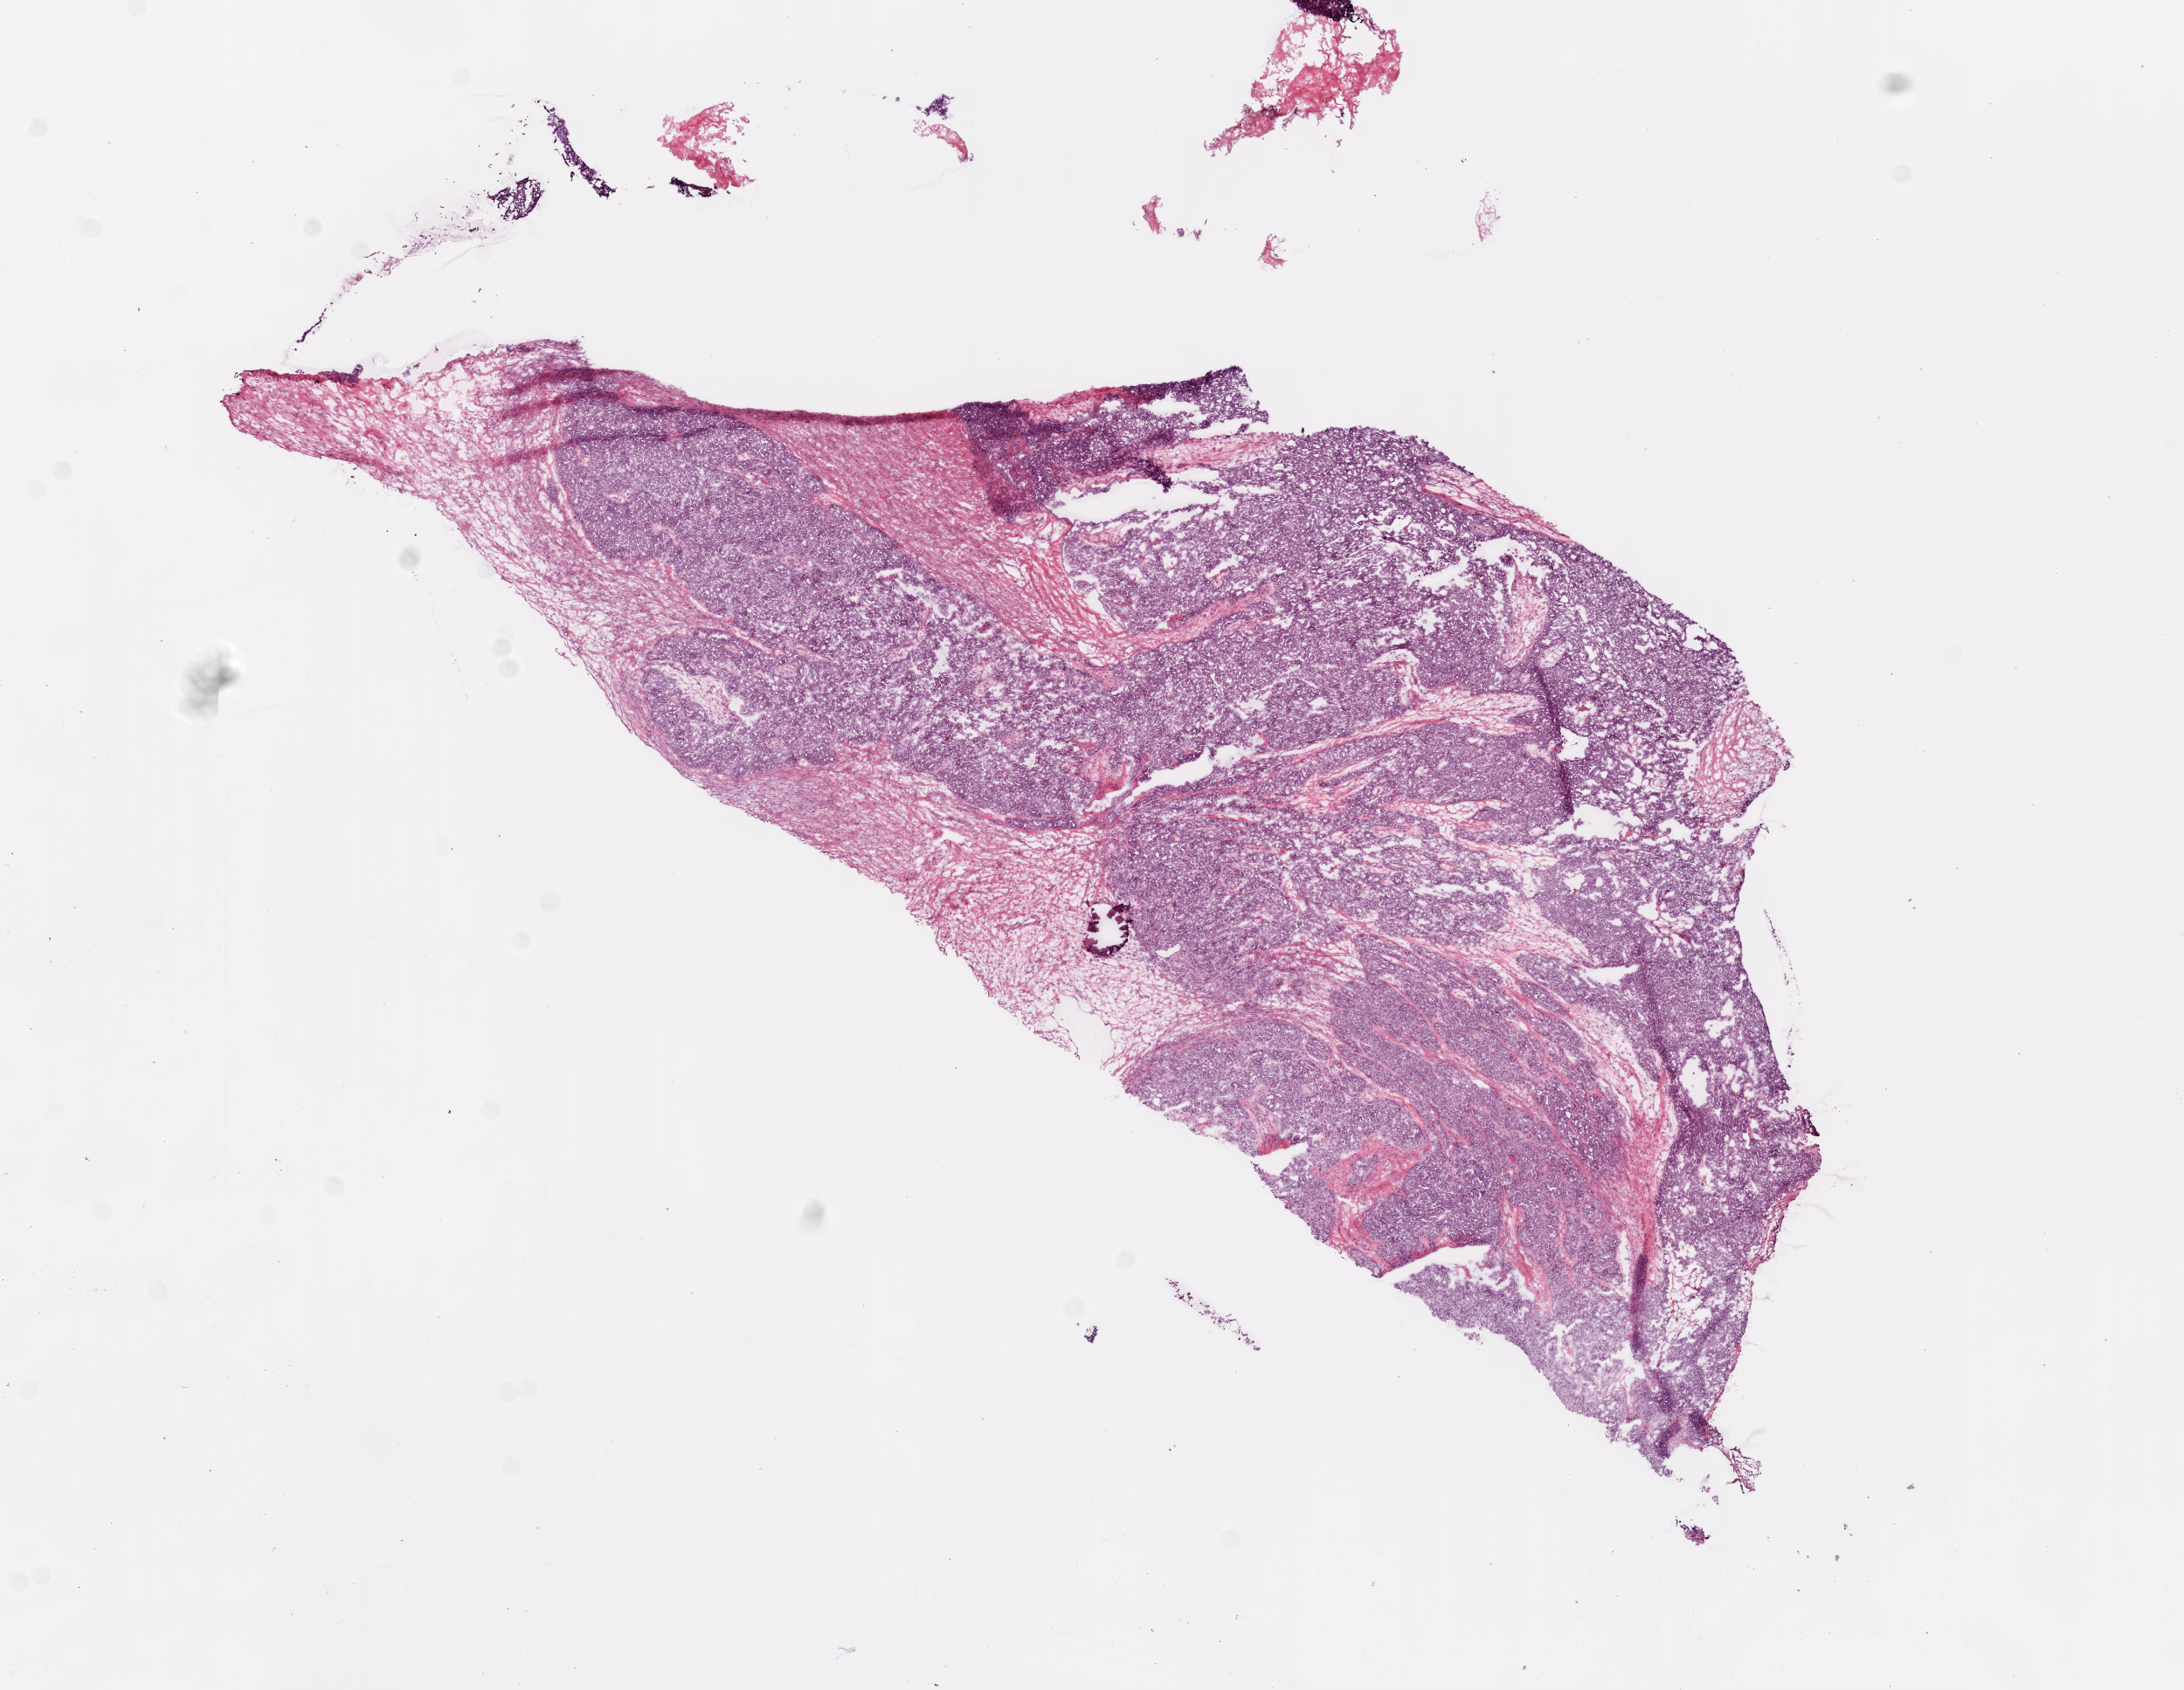
Hematoxylin and eosin (H&E) stained whole-slide image — shown as a low-resolution overview of the whole scanned area (about 10.0 x 7.8 mm), frozen section, primary tumour sample from the ovary. Female patient; age at initial diagnosis 51 years. Histologic grade: G3 (poorly differentiated). Pathologist review of this section (percent, as recorded): tumour cells 90%, tumour nuclei 90%, normal cells 0%, stromal cells 10%, necrosis 0%.
- FIGO stage: IIIC
- laterality: bilateral
- diagnosis: Serous cystadenocarcinoma, NOS